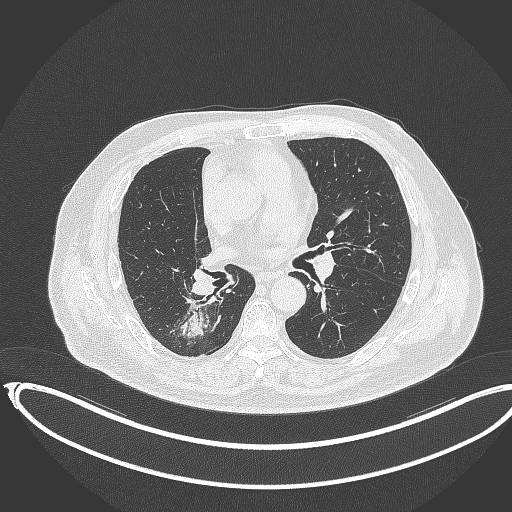
Chest CT, one axial slice; slice 185 of 403 in the series (ordered by position); 120 kVp; lung window (W 1500 / L -600 HU); 1 mm slice thickness; 512 × 512 image matrix, field of view 436 × 436 mm. Male patient, age 68 years. Case-level facts recorded for this patient, not image findings: clinical TNM (as recorded): T2a N0 M0.
Structures marked on this image (bounding box drawn by a radiologist):
- lung tumour (recorded histology: adenocarcinoma): bounding box [x1, y1, x2, y2] px = [170, 298, 219, 335]